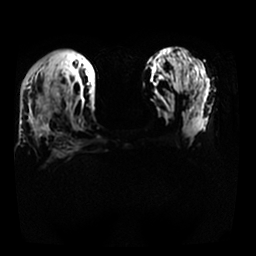
Breast MRI, one axial slice; slice 14 of 25 in the series (ordered by position); diffusion-weighted series; image 2 of 4 stored at this slice position (different b-values; order by instance number); 1.5 T; 256 × 256 image matrix, field of view 340 × 340 mm. Female patient.
Structures marked on this image (expert manual segmentation):
- tumour on diffusion-weighted imaging: bounding box <34,82,60,133> (left, top, right, bottom; pixels)